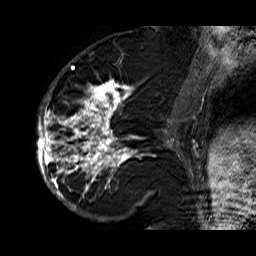
Breast MRI (dynamic contrast-enhanced), one sagittal slice; slice 25 of 60 in the series (ordered by position); dynamic contrast-enhanced series, time point 2 of 6 at this slice position (early post-contrast); 1.5 T; TE 6.3 ms, TR 32.9 ms; 256 × 256 image matrix. Female patient. From the clinical record (not read from this slice): setting: breast cancer imaged before/during neoadjuvant chemotherapy; receptor status: HR-positive, HER2-negative.
Structures marked on this image (semi-automatically segmented with operator editing):
- analysis volume of interest (the breast-tissue region the enhancement analysis was run in; not a lesion): bounding box (x1, y1, x2, y2) in pixels: (36, 74, 176, 210)
- tumour enhancement mask (voxels above the 100 % enhancement threshold inside the analysis volume of interest): (36, 77, 176, 209)